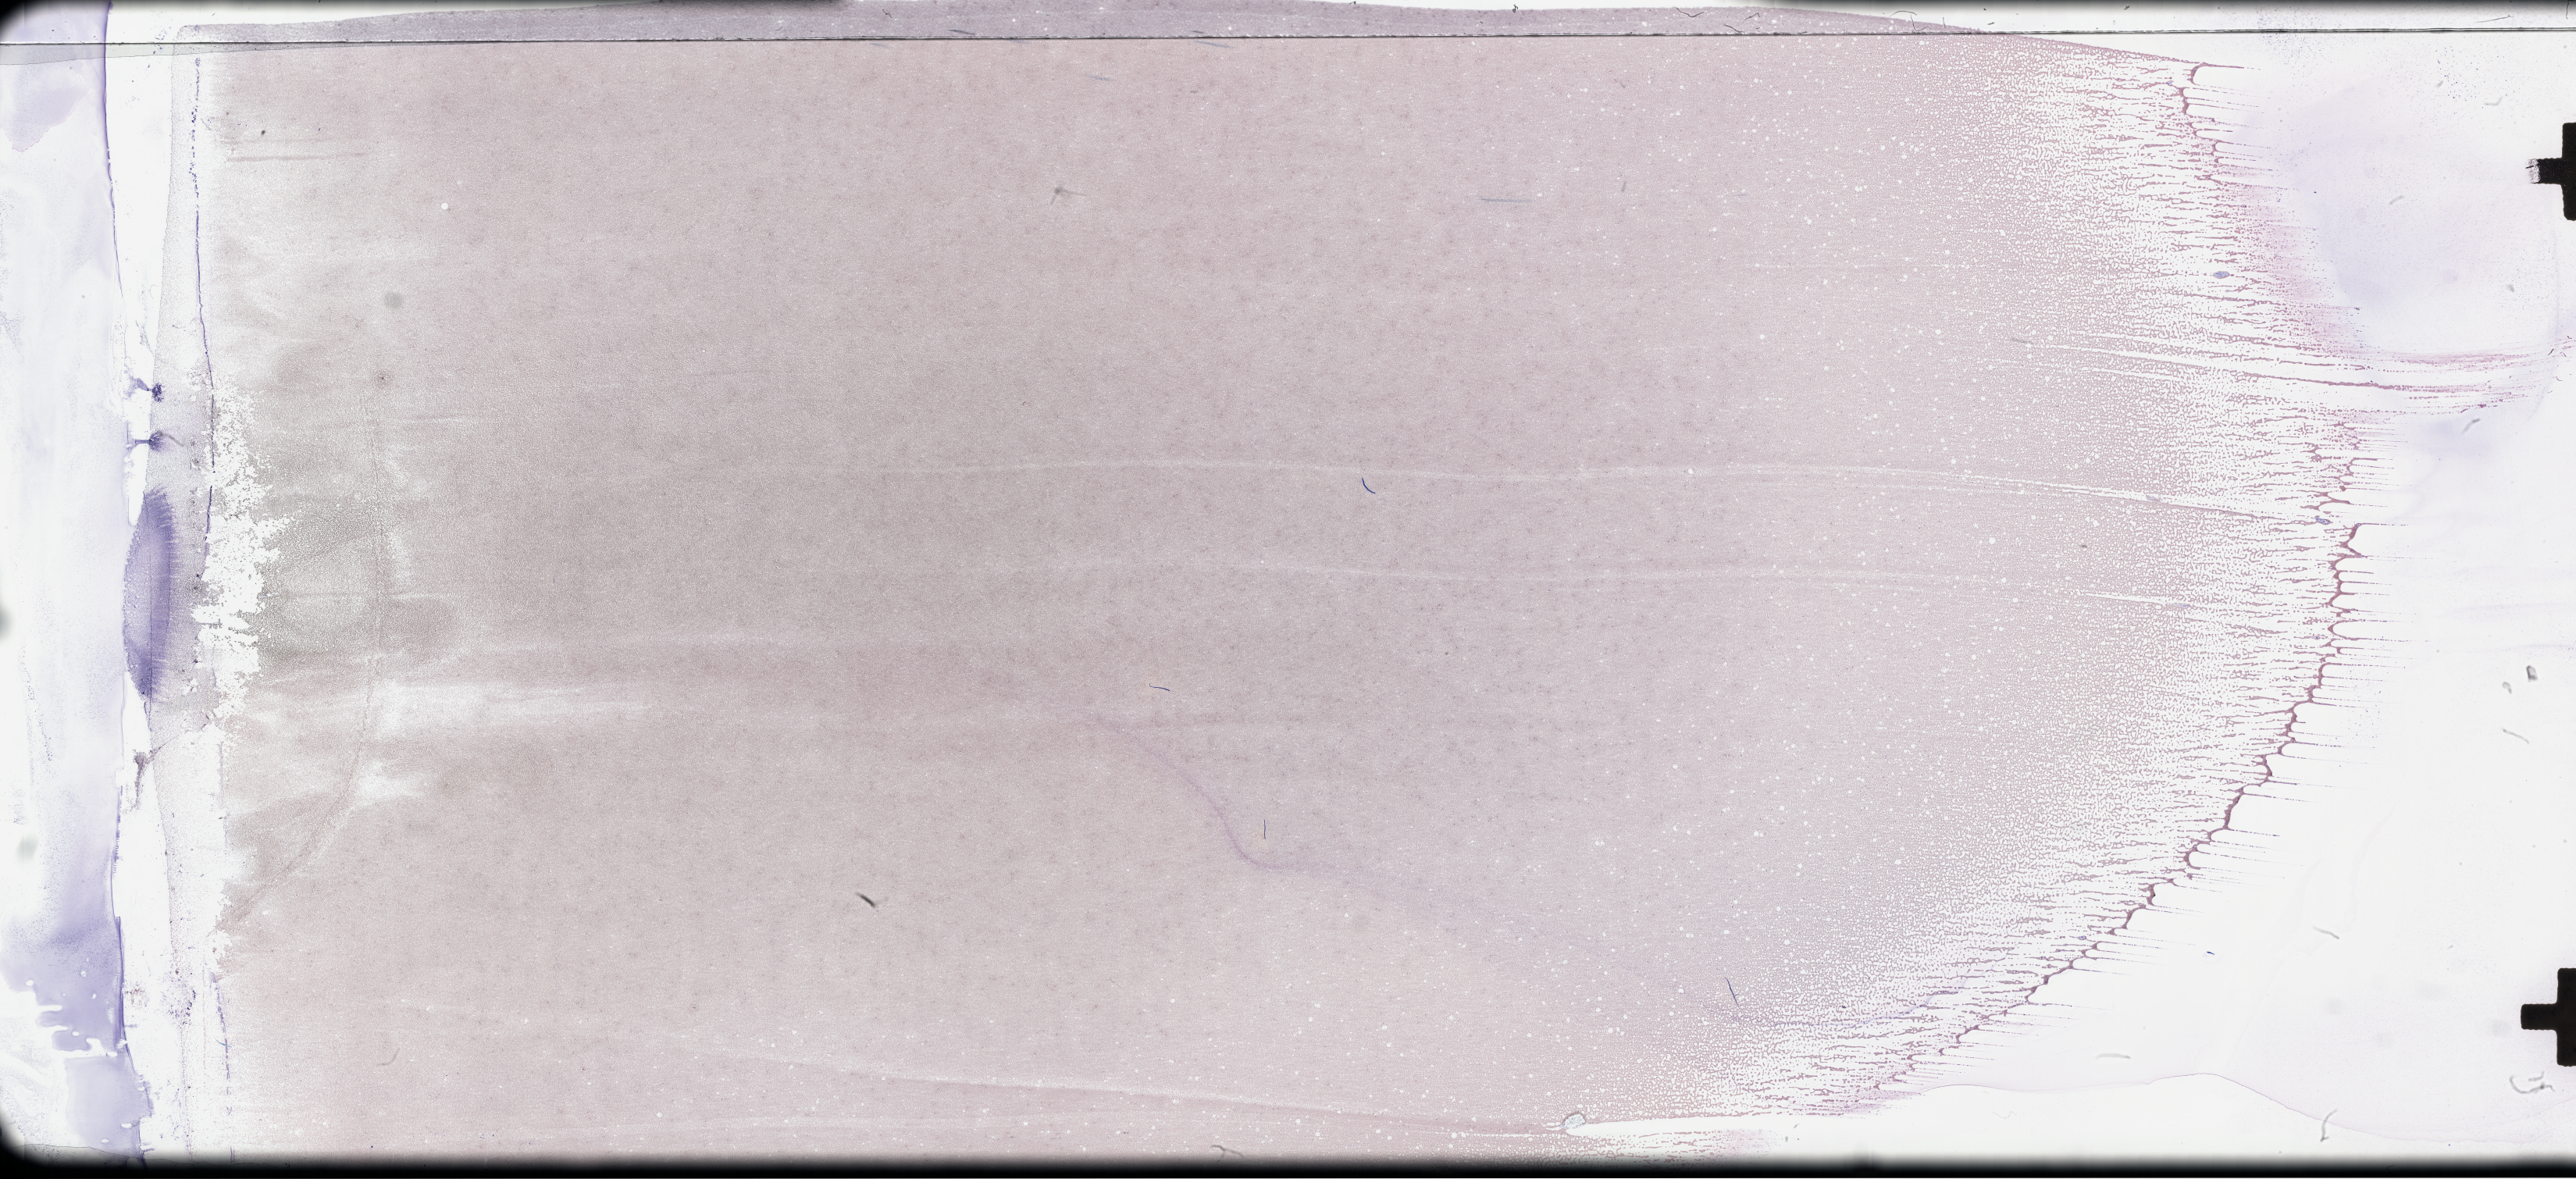
Wright-Giemsa-stained whole blood smear, whole-slide image, shown as a low-resolution overview of the whole scanned area (about 53.3 x 24.4 mm). EDTA-anticoagulated smear. Collected on treatment. Patient sex: male.
Patient diagnosis: Plasma Cell Myeloma.